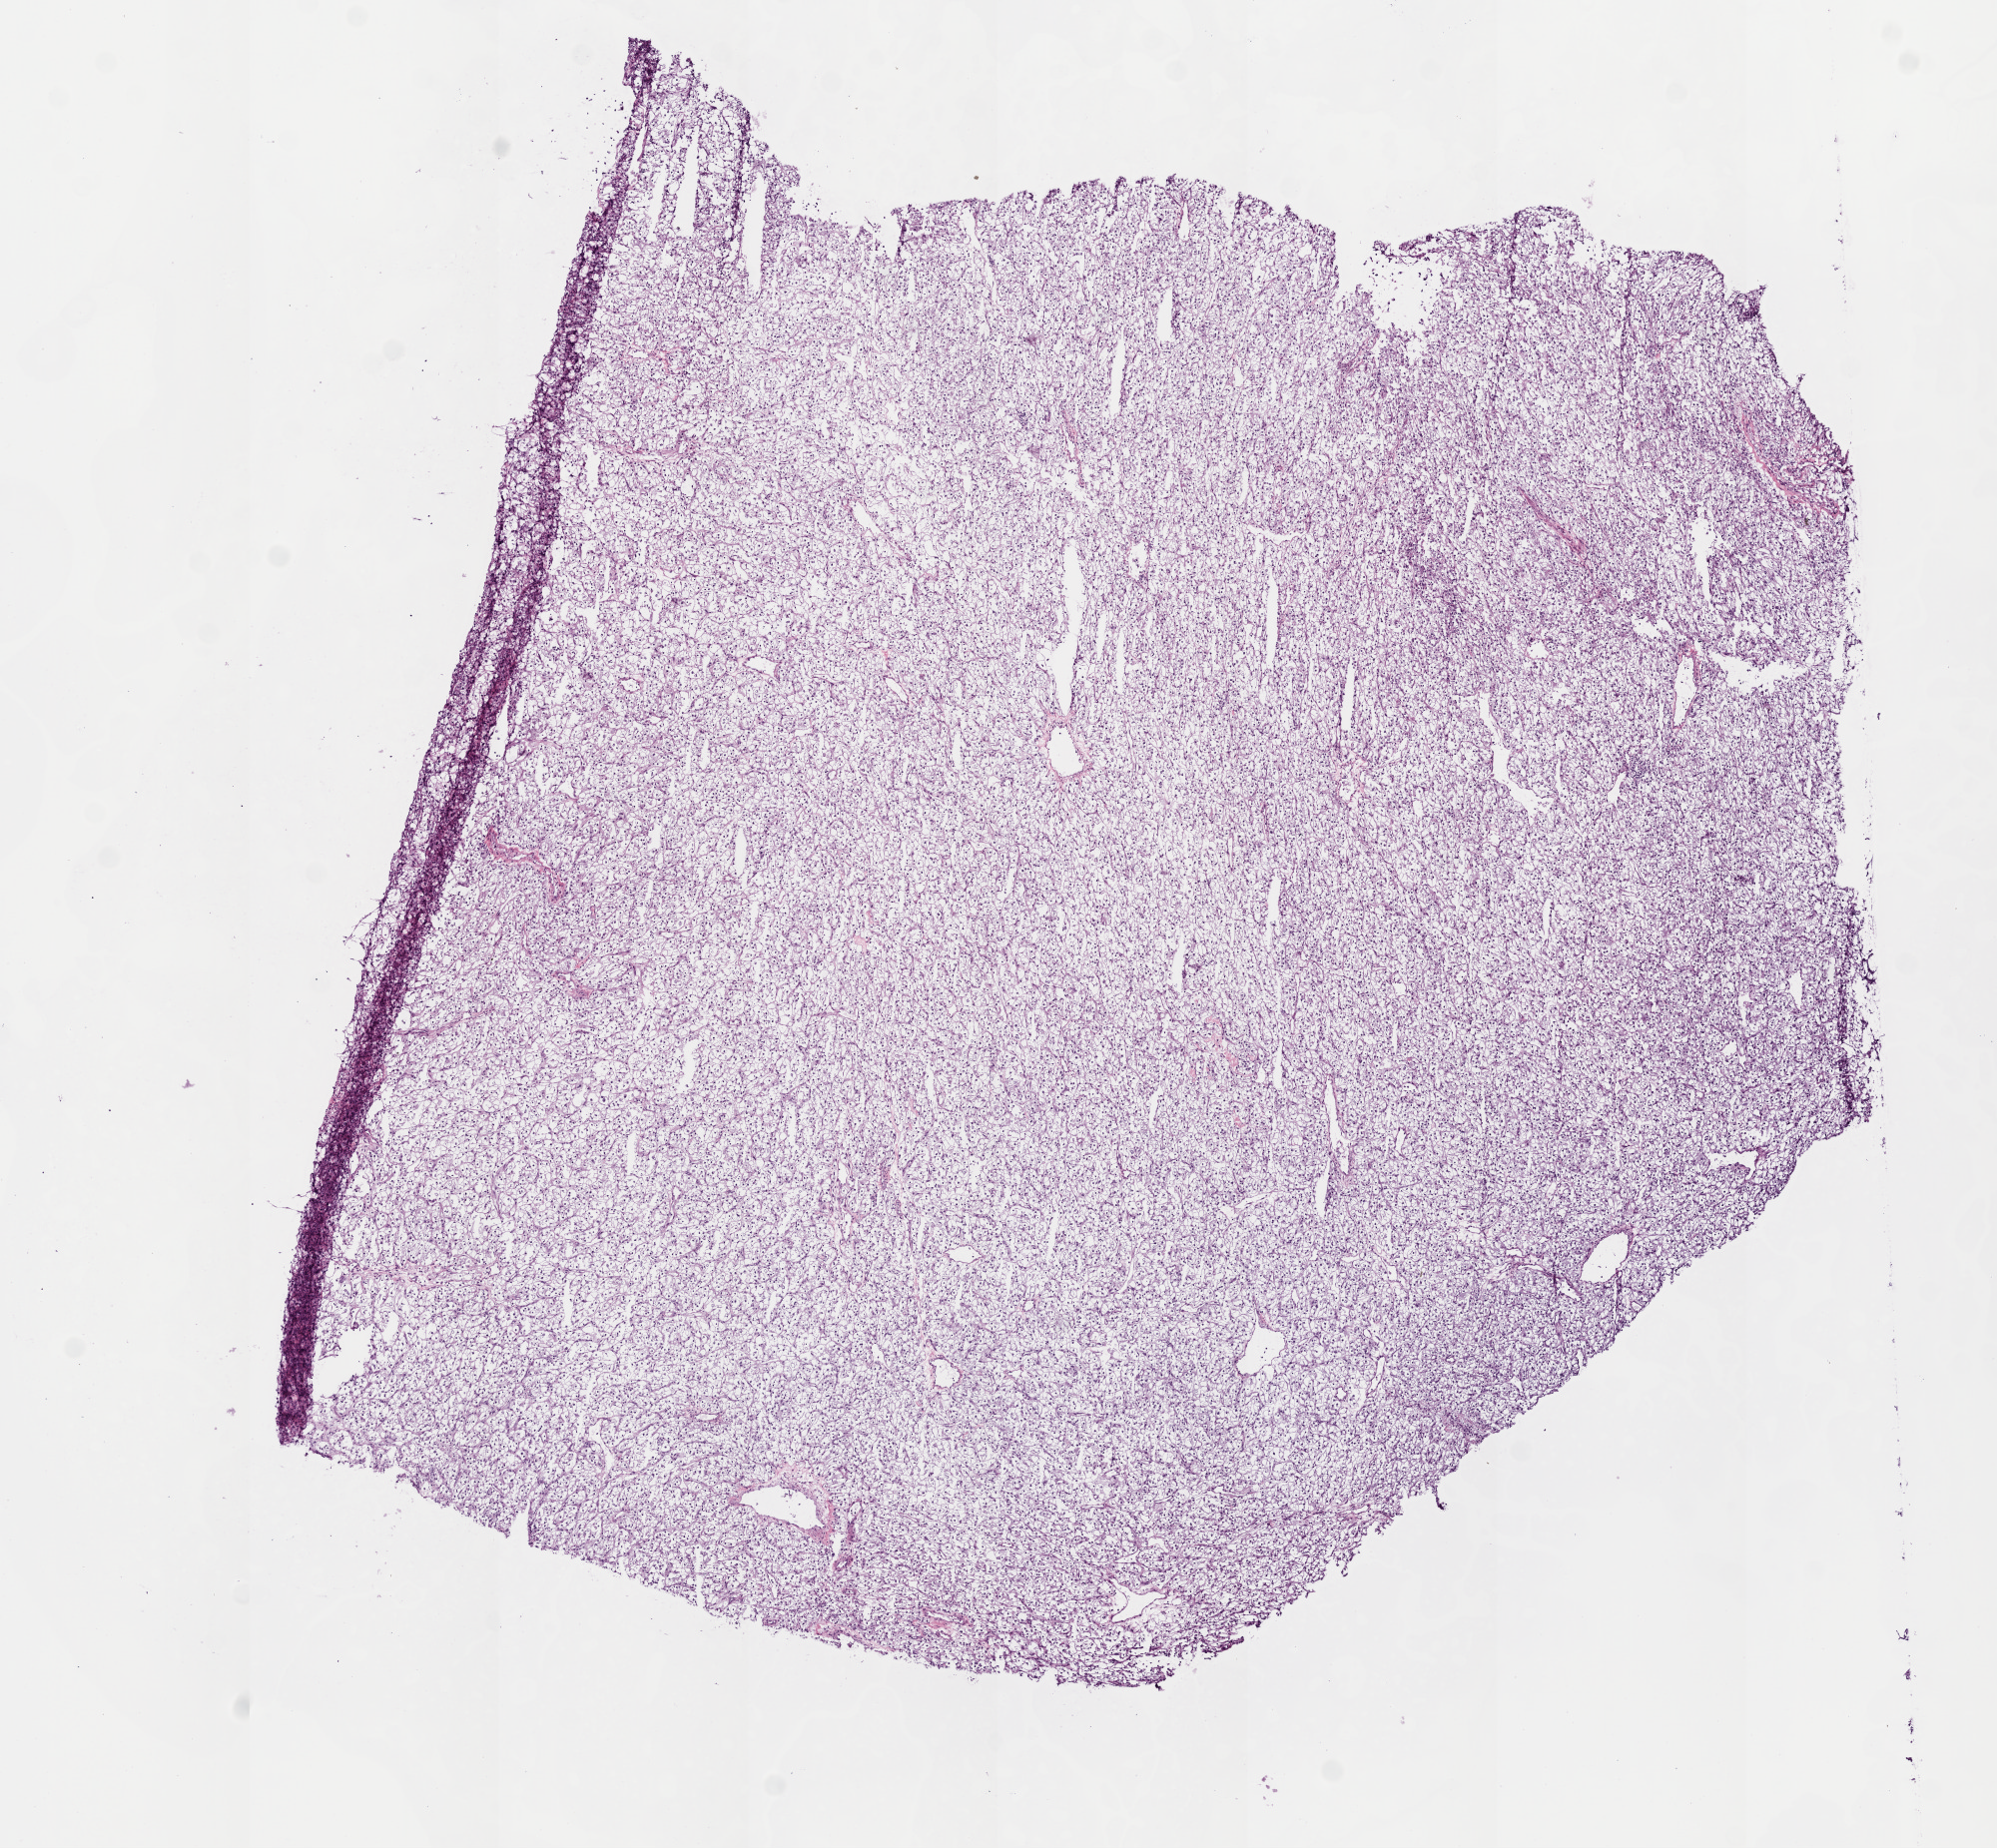
H&E whole-slide image, shown as a low-resolution overview of the whole scanned area (about 8.0 x 7.4 mm, slide scanned at 20x), frozen section from the top of the tissue portion, sample: primary tumour, kidney. Male, age 56 years at initial diagnosis. Histologic grade: G2 (moderately differentiated). Composition of this section per pathologist review: tumour cells 95%, tumour nuclei 90%, normal cells 0%, stromal cells 5%, necrosis 0%. Inflammatory infiltration, as recorded: lymphocyte infiltration 2%, monocyte infiltration 0%, neutrophil infiltration 0%.
Pathologic diagnosis: Clear cell adenocarcinoma, NOS. AJCC pathologic stage: IV. Laterality: right. Lymph nodes positive (case pathology): 0 of 2 examined.